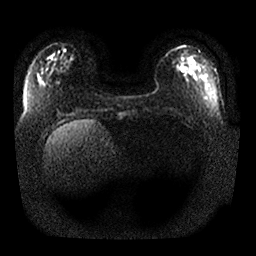
Breast MRI, one axial slice. Slice 6 of 25 in the series (ordered by position). Diffusion-weighted series; image 2 of 4 stored at this slice position (different b-values; order by instance number). 1.5 T. 4 mm slice thickness. 256 × 256 image matrix. Female patient.
Structures marked on this image (manually delineated by an expert):
- tumour on diffusion-weighted imaging: box from (x=181, y=63) to (x=185, y=71) px